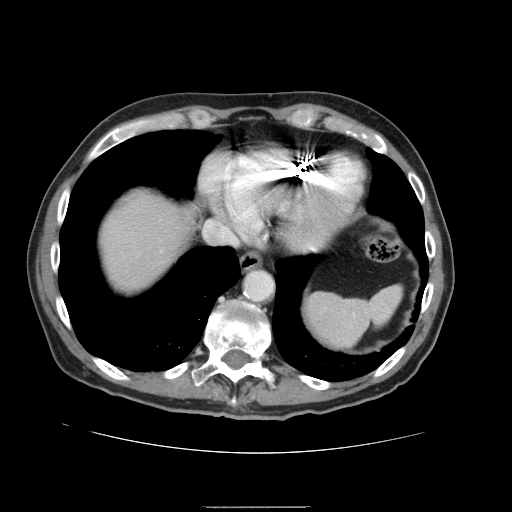
Contrast-enhanced abdominal CT, one axial slice; position 135 of 168 along the scan axis; intravenous contrast given; soft-tissue window (W 400 / L 40 HU); 512 × 512 image matrix, field of view 386 × 386 mm. Male patient, age 74 years. Case-level facts recorded for this patient, not image findings: diagnosis: colorectal cancer liver metastases, imaged before liver resection; multiple liver metastases: no; largest metastasis: 14.5 cm; disease in both lobes: yes.
Outlined on this slice (expert manual segmentation):
- liver: bounding box (x1, y1, x2, y2) in pixels: (96, 187, 199, 296)
- planned liver remnant (the part of the liver to remain after resection): (96, 186, 199, 297)